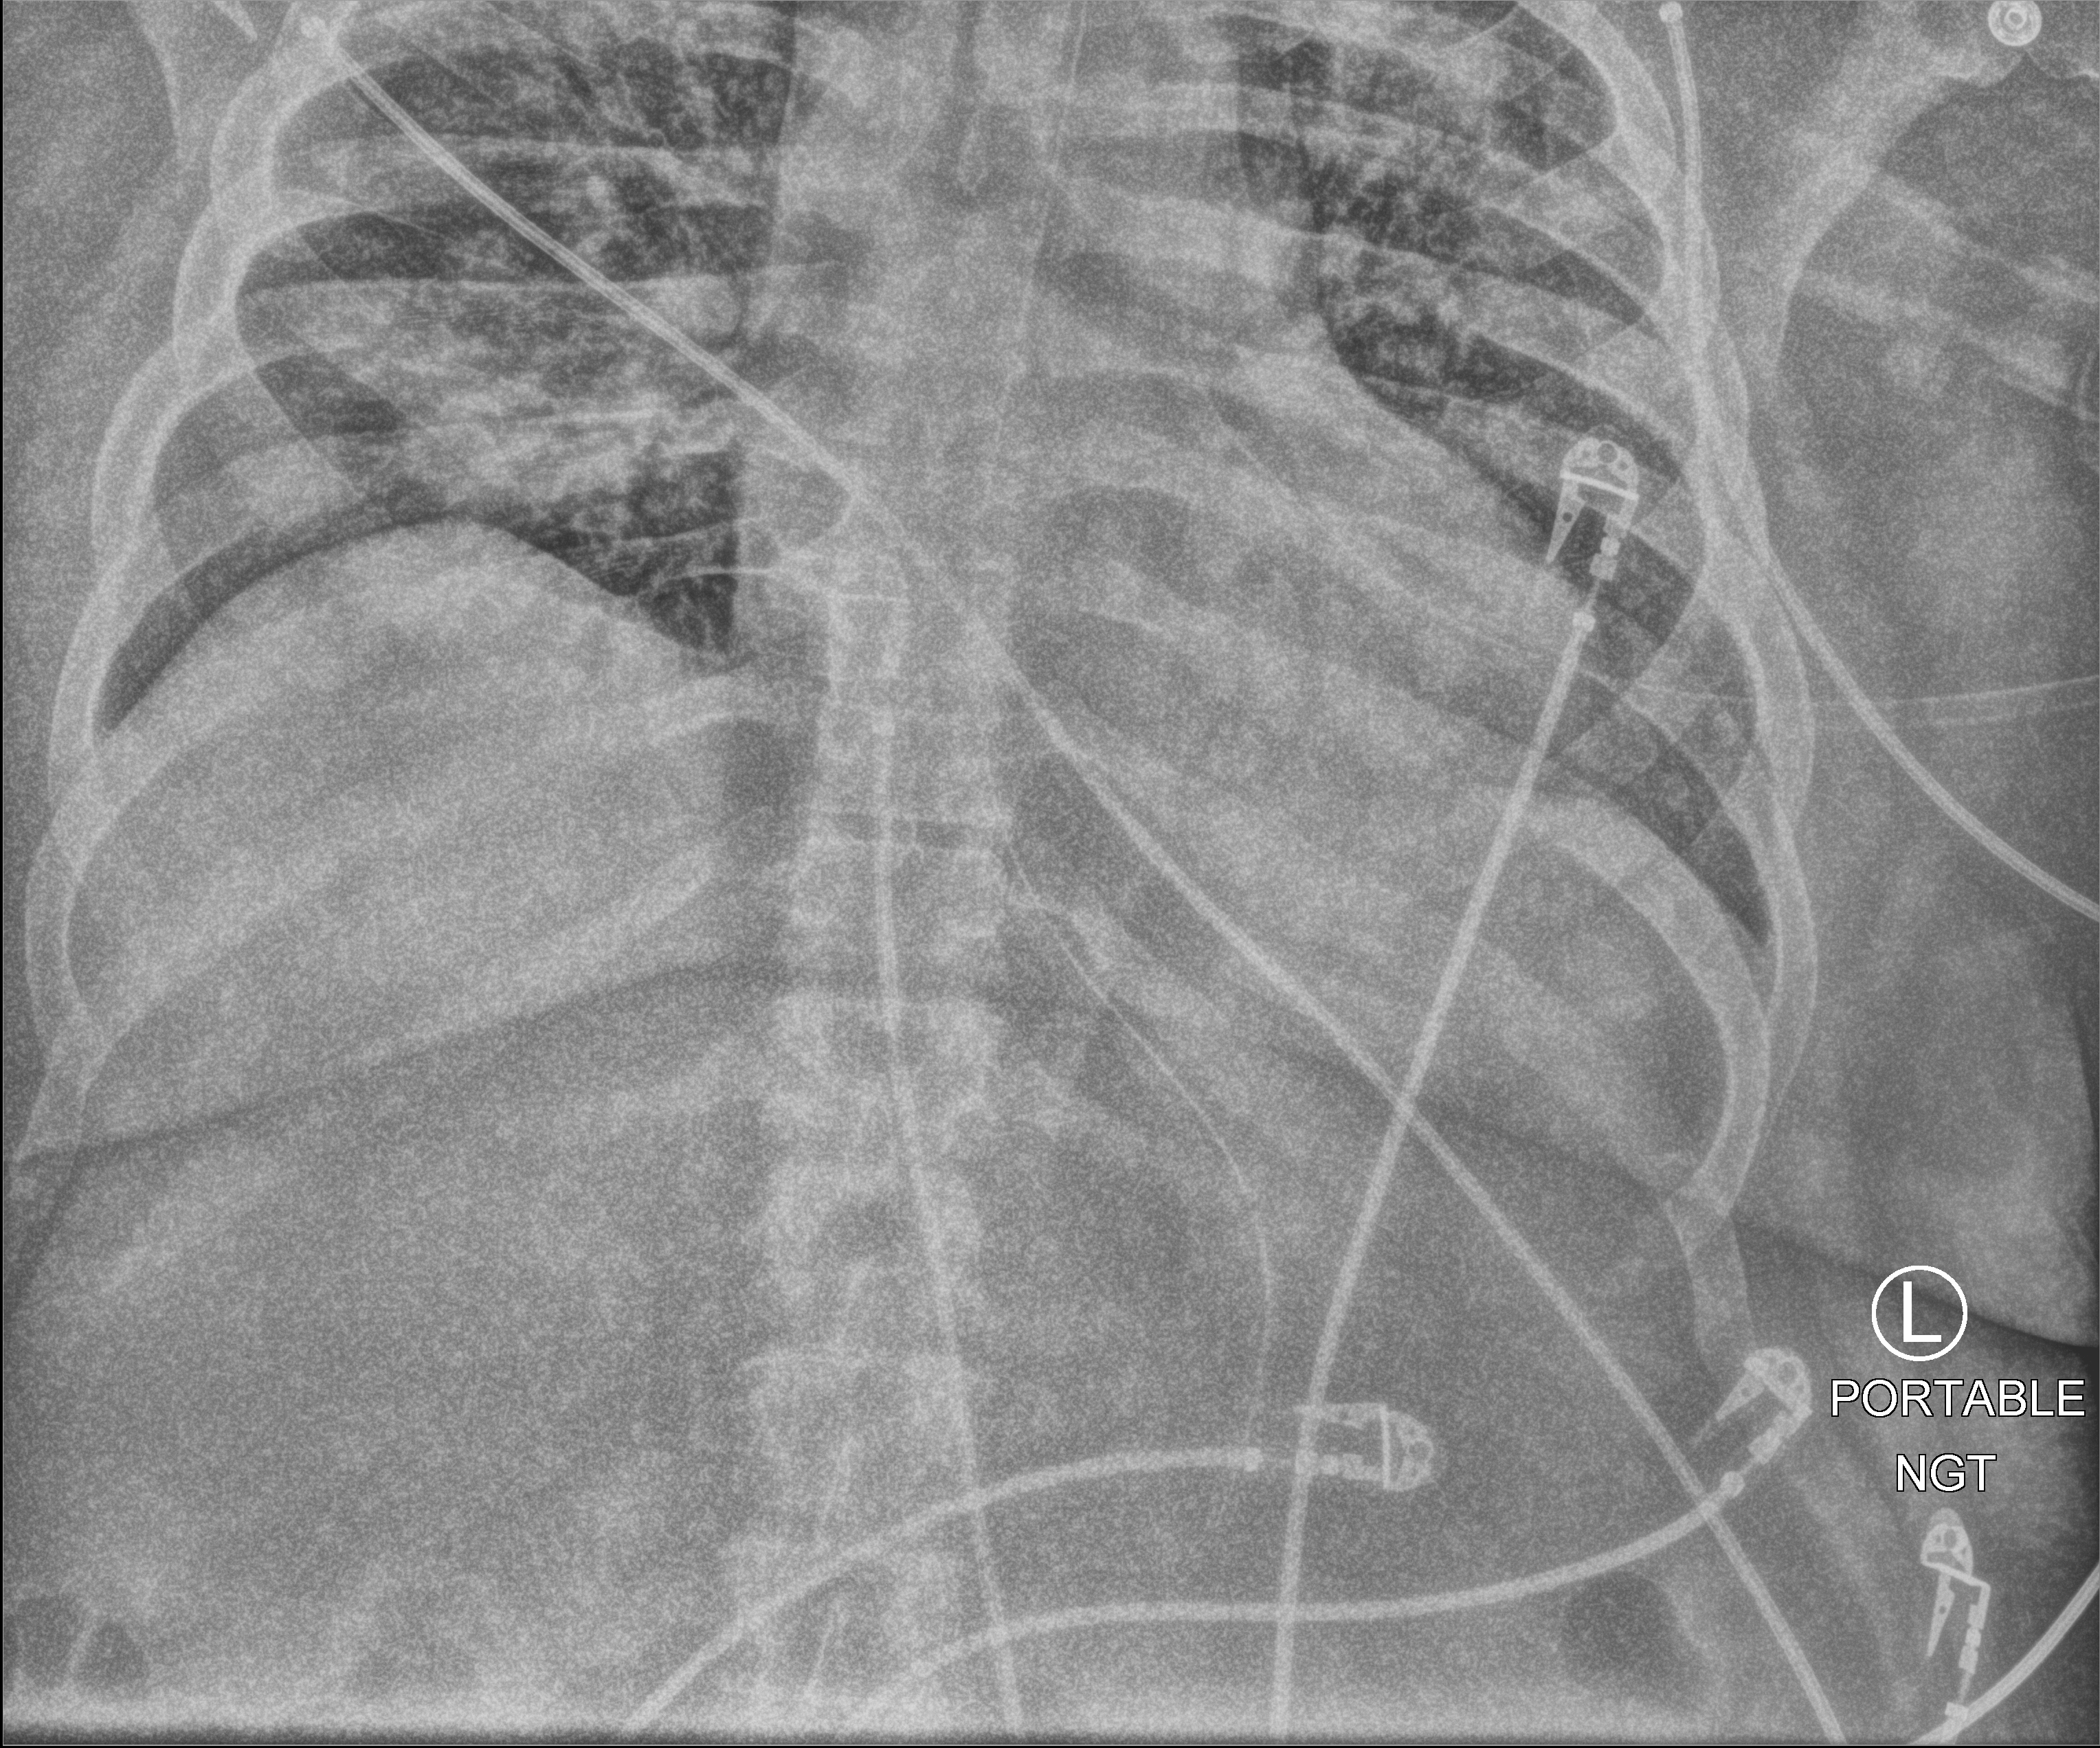
Bedside chest radiograph (computed radiography), anteroposterior (AP) projection. Adult patient hospitalised with COVID-19, age 18–59 years.
Hospital-stay facts (about this admission, not read from this image; timing relative to this image not recorded): admitted to intensive care during this hospital stay: yes.